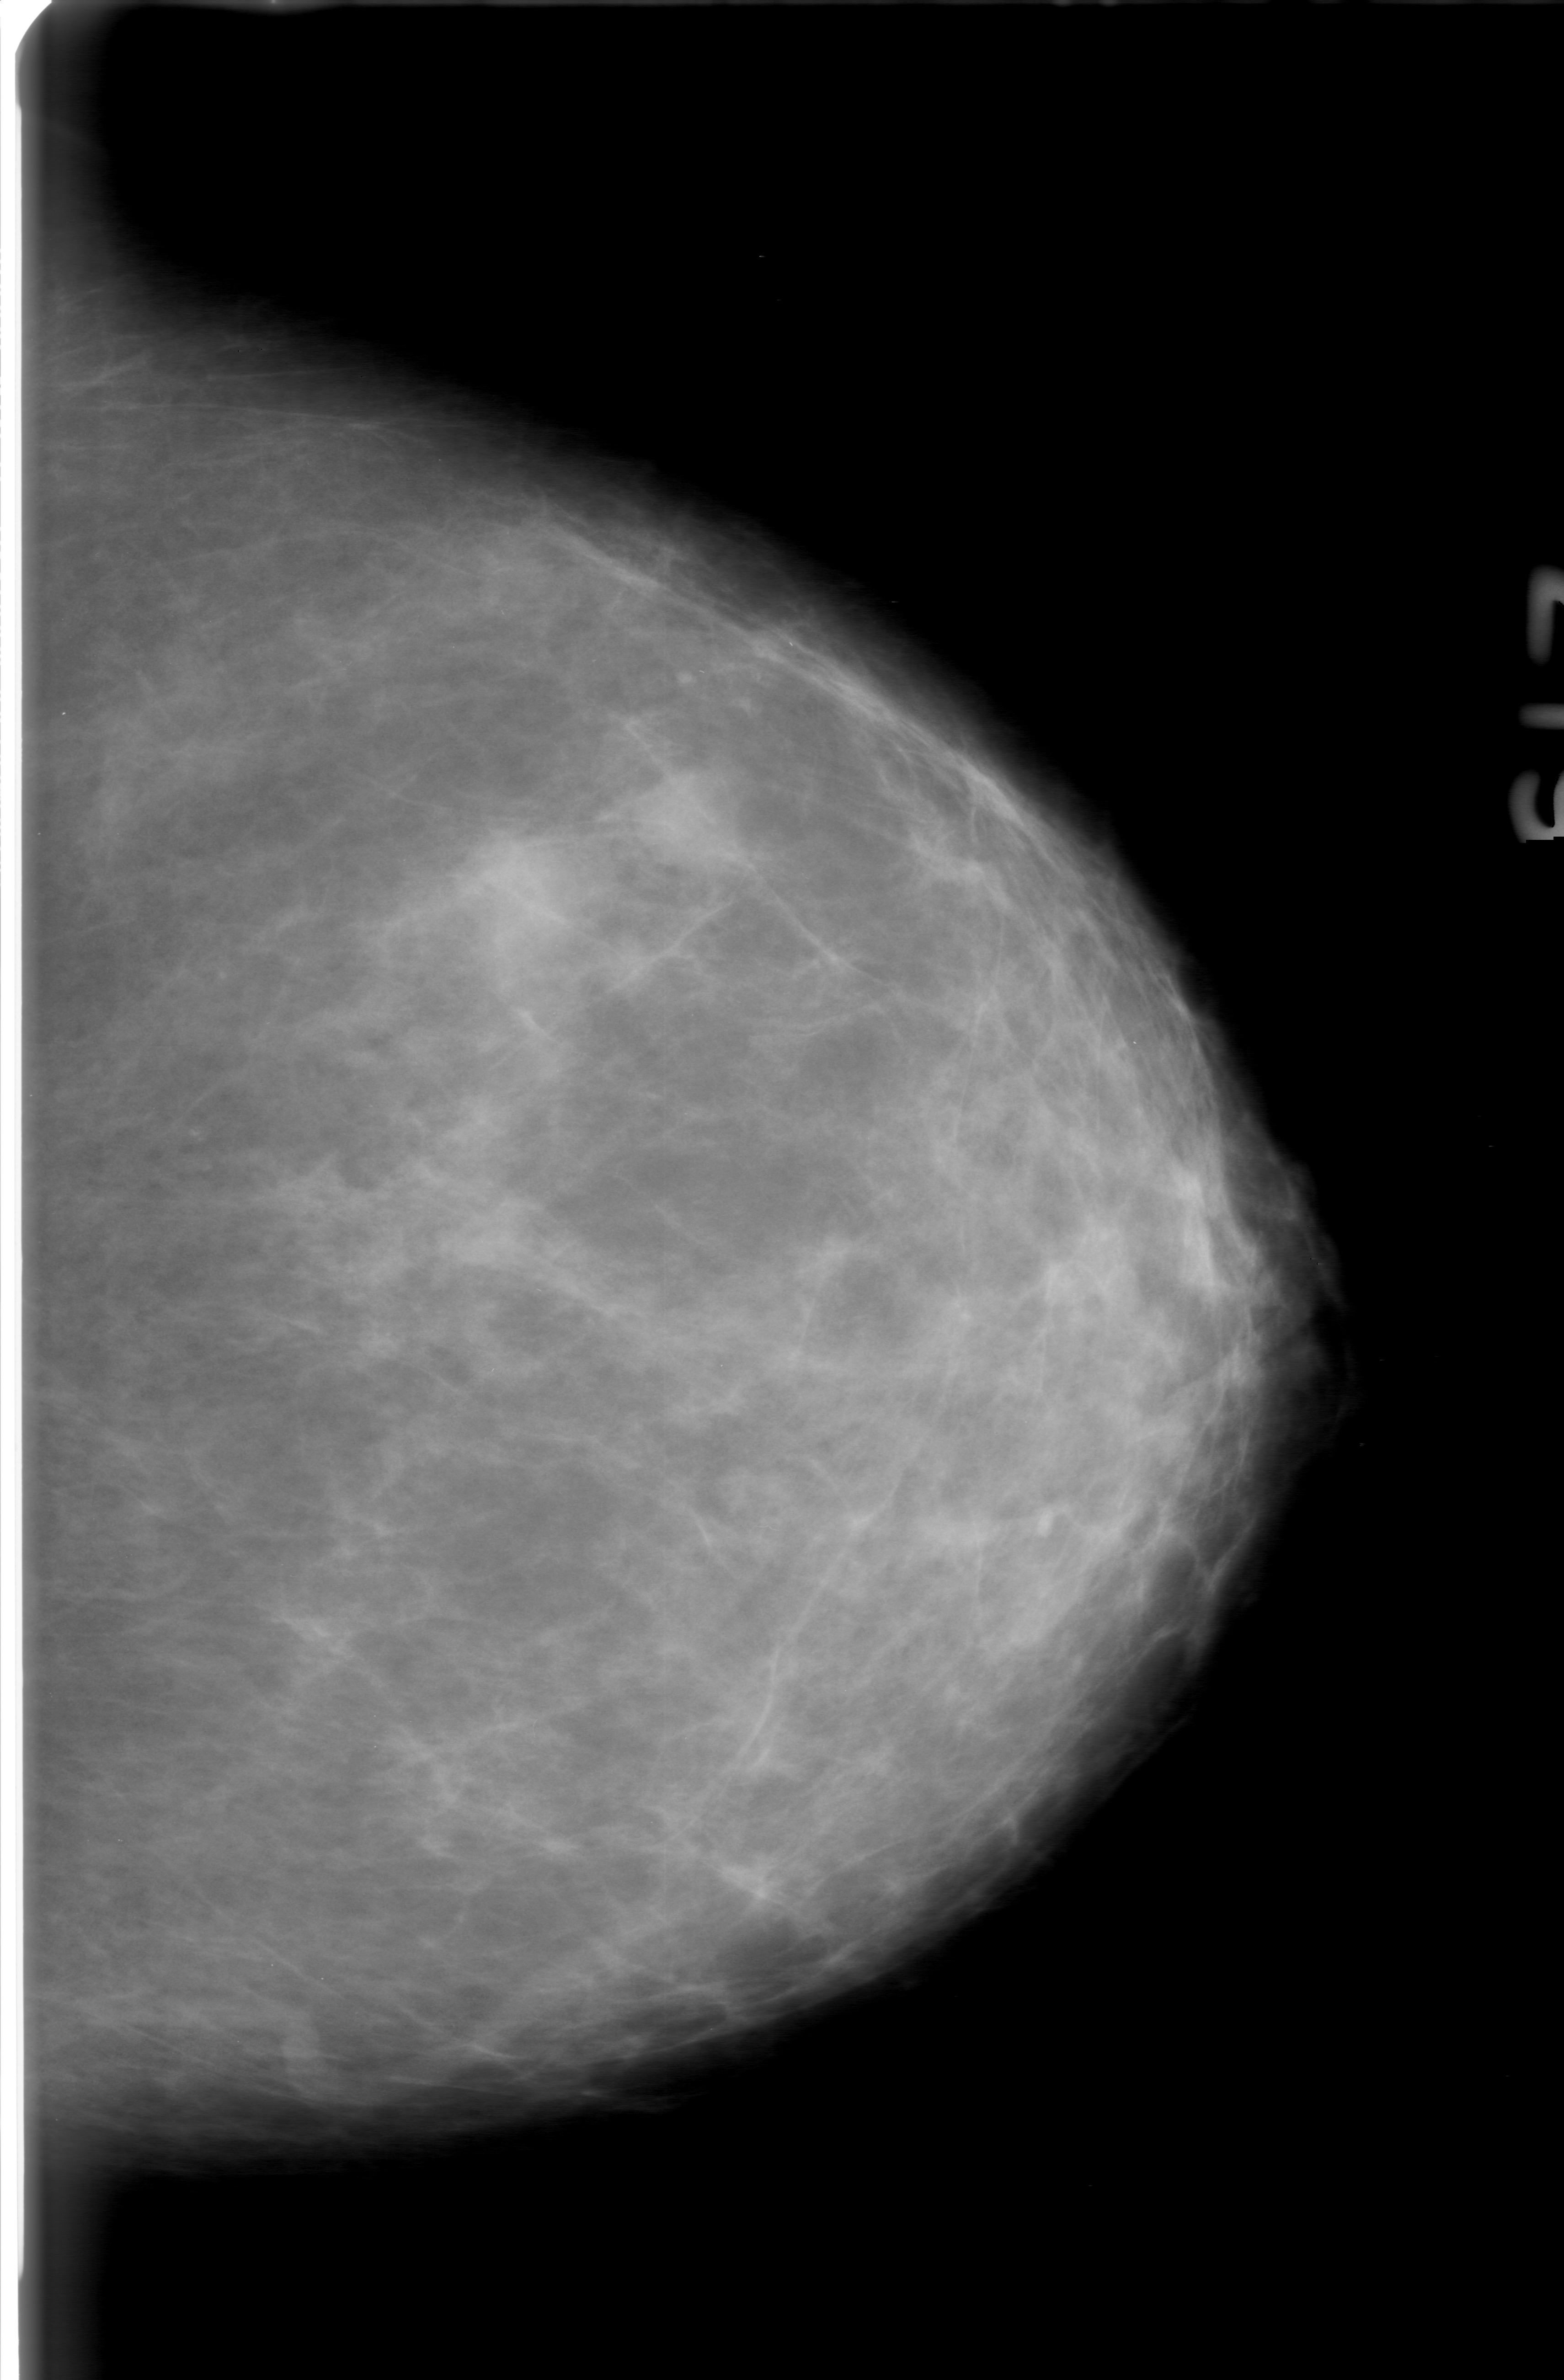
Mammogram (digitized film), left breast, craniocaudal (CC) view, breast composition: scattered fibroglandular densities (BI-RADS density category 2 of 4).
Finding: mass, shape lobulated, margins obscured; BI-RADS assessment category 0 (incomplete: needs additional imaging); subtlety rating 4 on a 1 (subtle) to 5 (obvious) scale; pathology result (as recorded, not read from the image): benign.